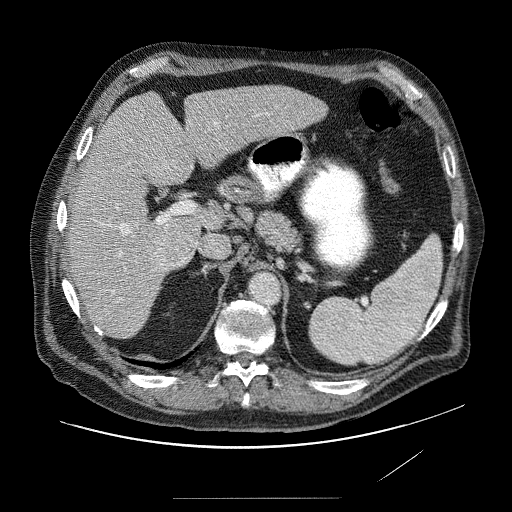
Contrast-enhanced abdominal CT (liver protocol), one axial slice. Reconstruction kernel STANDARD. Soft-tissue window (W 400 / L 40 HU). 2.5 mm slice thickness. 512 × 512 image matrix. From the clinical record (not read from this slice): diagnosis: hepatocellular carcinoma (patient treated with transarterial chemoembolisation; whether this scan precedes or follows treatment is not stated here); TNM stage (as recorded): Stage-IVA; Child-Pugh class: A.
Annotated regions visible in this slice (semi-automatically segmented with operator editing):
- liver parenchyma outside the tumour (the mass and vessels are separate outlines, so this box may not span the whole liver): box from (x=62, y=84) to (x=330, y=336) px
- mass: (x=150, y=151)–(x=194, y=268)
- liver vessels: (x=100, y=115)–(x=259, y=302)